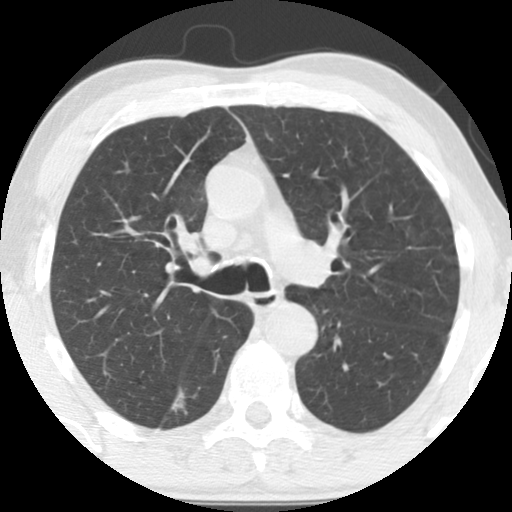
Low-dose screening chest CT, one axial slice; slice 93 of 135 in the series (ordered by position); lung window (W 1500 / L -600 HU); 512 × 512 image matrix, field of view 300 × 300 mm.
Outlined on this slice (outlined manually by an expert reader):
- lesion 1 (tumor, lower lobe of right lung): box from (x=172, y=392) to (x=184, y=410) px